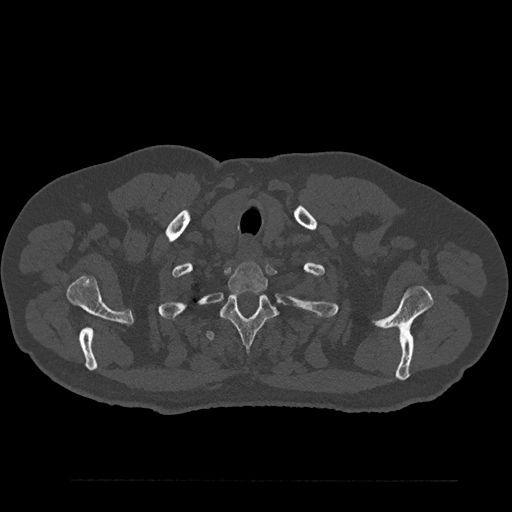
CT including the spine, one axial slice. Slice 723 of 797 in the series (ordered by position). 120 kVp. Bone window (W 1800 / L 400 HU). 512 × 512 image matrix, field of view 430 × 430 mm. Male patient, age 61 years. Case-level facts recorded for this patient, not image findings: primary cancer: prostate.
Annotated regions visible in this slice (semi-automatically segmented with operator editing):
- T1 vertebra: bounding box (x1, y1, x2, y2) in pixels: (227, 262, 268, 293)
- T2 vertebra: (221, 292, 277, 346)
- T3 vertebra: (205, 330, 291, 342)